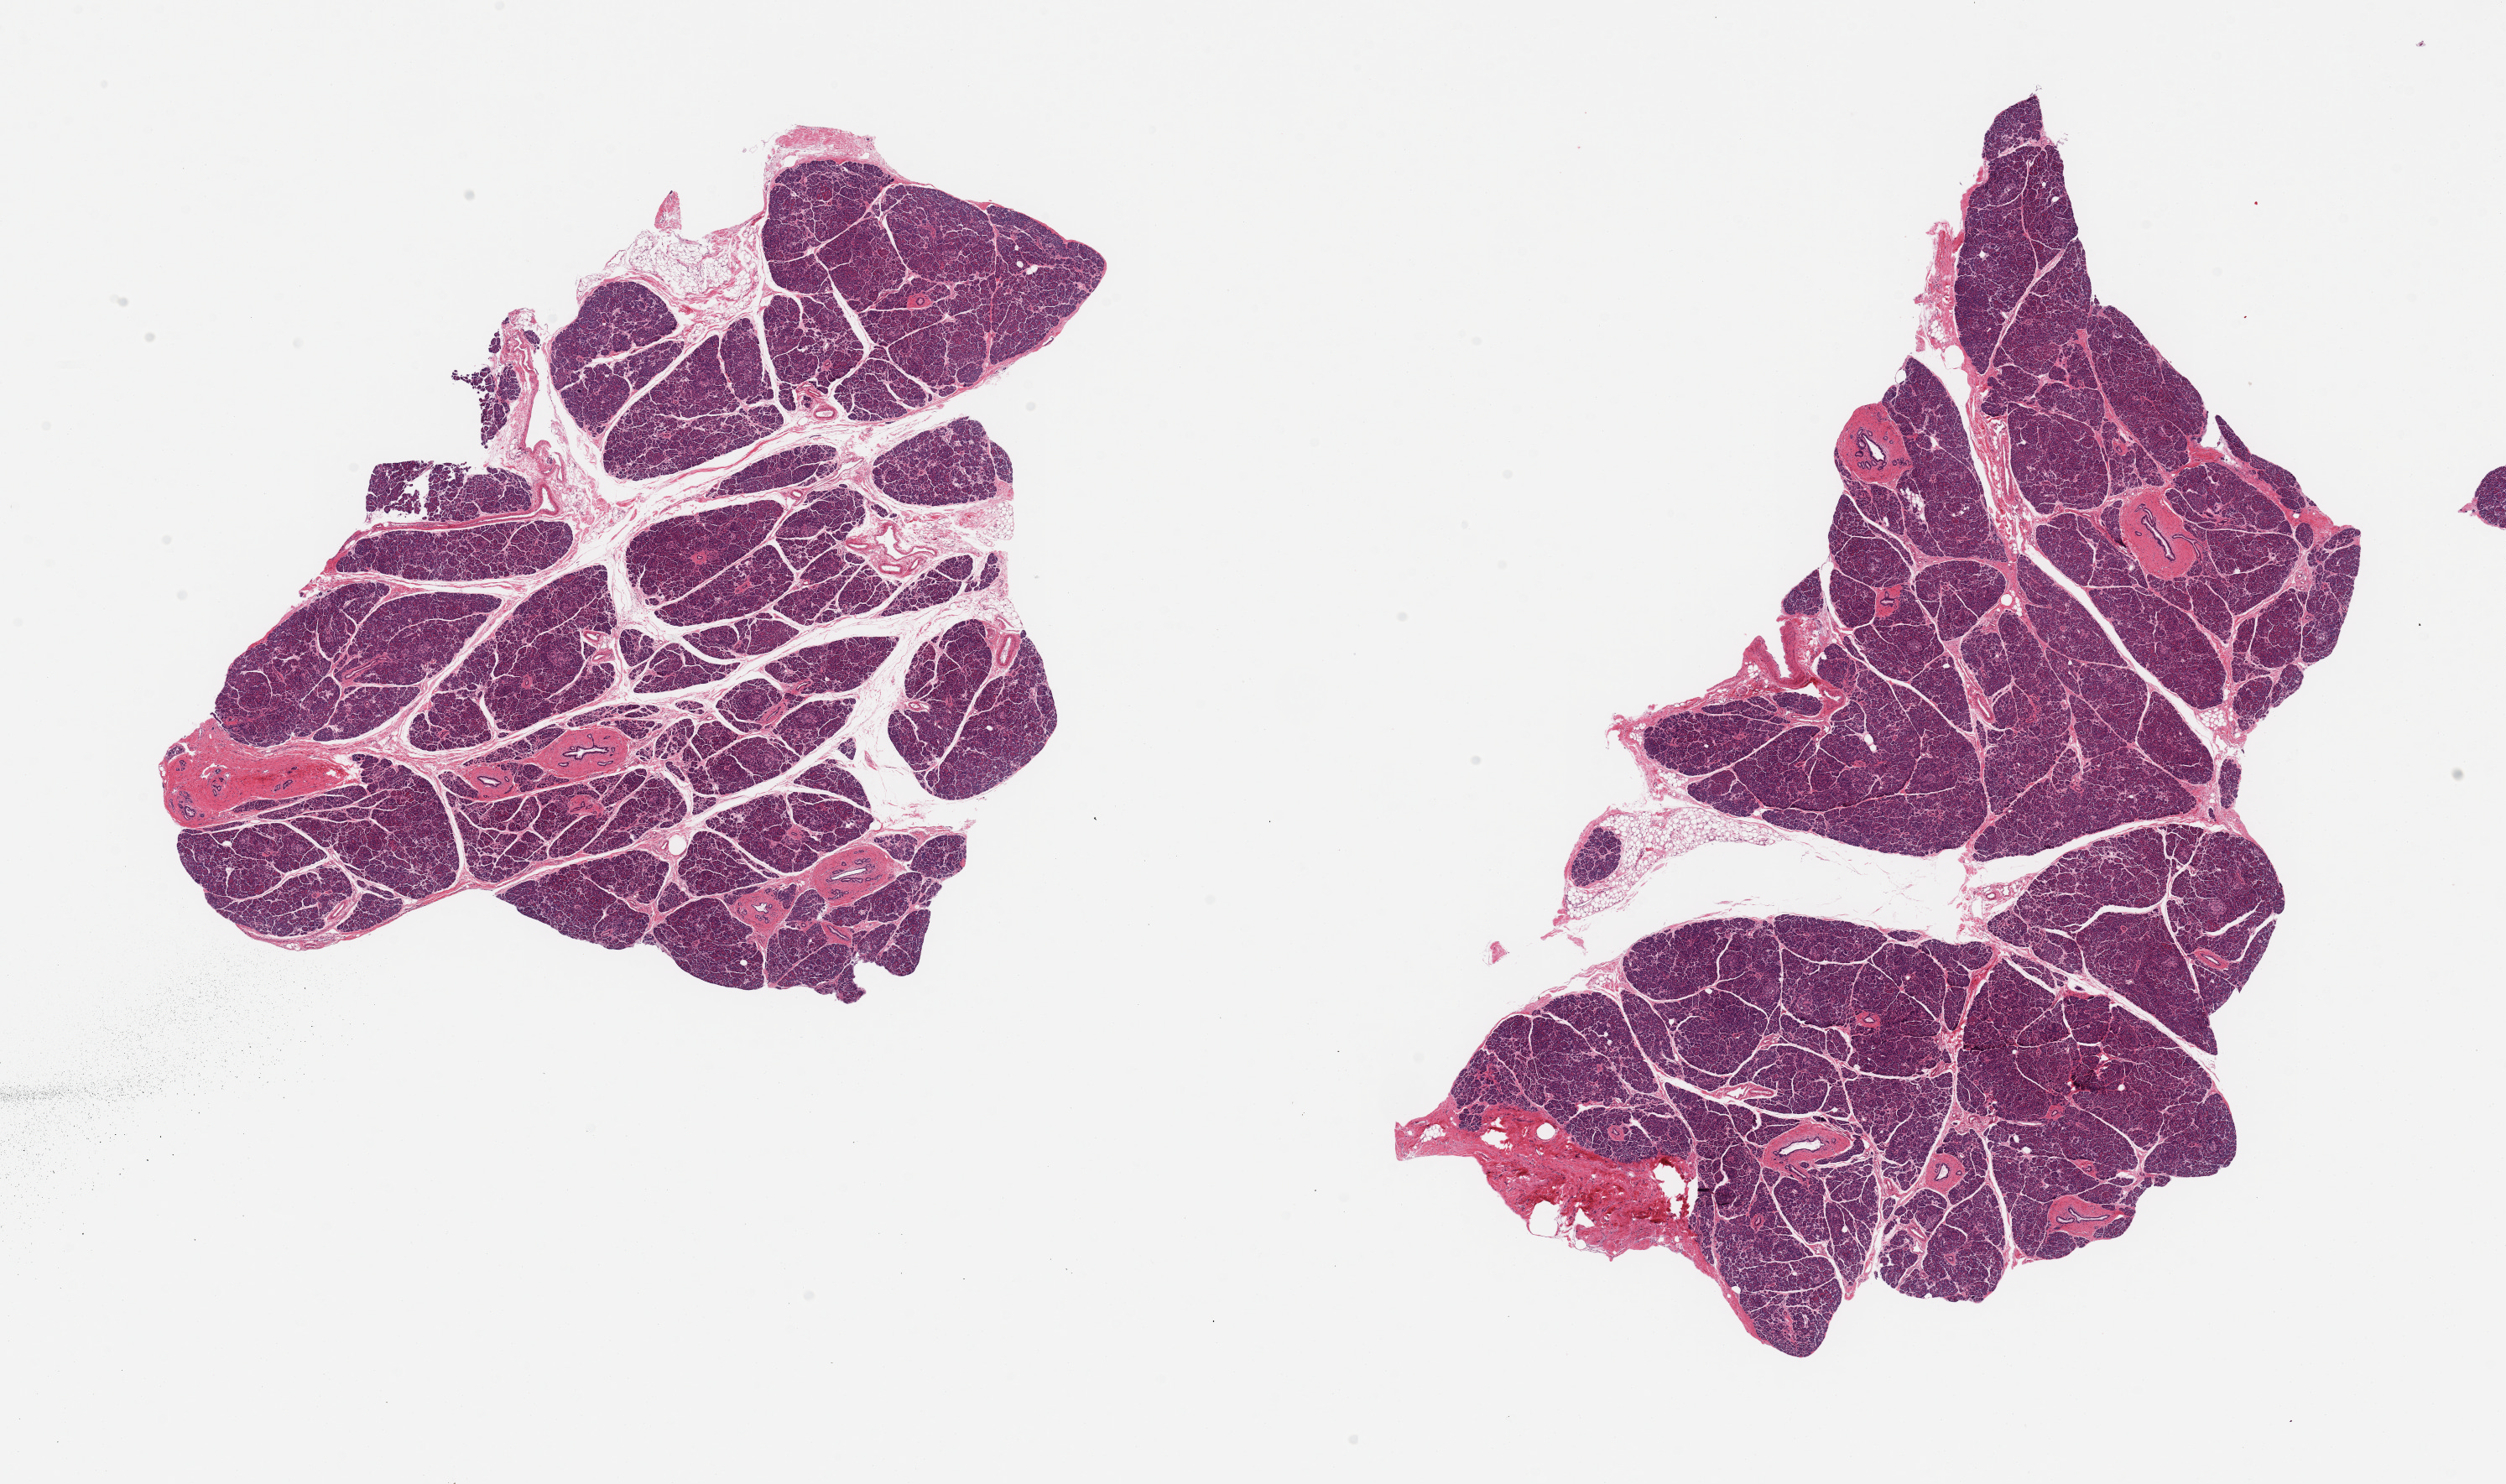
Digitized haematoxylin and eosin-stained section — whole scanned area (about 23.6 x 14.0 mm, from a 20x scan) shown as a low-resolution overview; PAXgene-fixed, paraffin-embedded tissue; section of pancreas (target tissue); tissue donor sample. Donor sex: male.
* review note (as recorded): 2 pieces; includes 5-10% fat